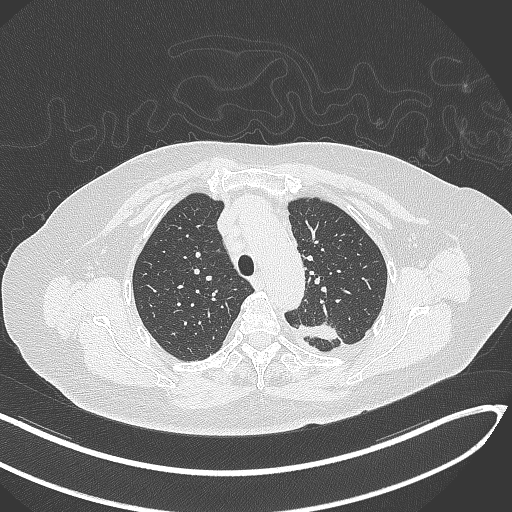
Chest CT, one axial slice. Position 241 of 270 along the scan axis. Lung window (W 1500 / L -600 HU). 1 mm slice thickness. 512 × 512 image matrix, field of view 400 × 400 mm. Patient: female, 76 years. Case-level facts recorded for this patient, not image findings: clinical TNM (as recorded): T1c N0 M0.
Structures marked on this image (rectangle marked by the reading radiologist):
- lung tumour (recorded histology: adenocarcinoma): bounding box (x1, y1, x2, y2) in pixels: (298, 323, 341, 345)